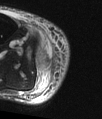
MRI of an extremity soft-tissue mass, one axial slice. Position 12 of 48 along the scan axis. T2-weighted fat-saturated. MR volume resampled by the dataset authors to the PET/CT grid (not the native acquisition matrix). 3.27 mm slice thickness. 102 × 119 image matrix, field of view 100 × 116 mm. Male patient. From the clinical record (not read from this slice): histological type: pleiomorphic liposarcoma; grade: high; site of the primary tumour: right calf.
Structures marked on this image (expert contour drawn on MRI and transferred to this co-registered scan by the dataset authors):
- gross tumour volume including surrounding oedema: bounding box (x1, y1, x2, y2) in pixels: (37, 51, 52, 72)